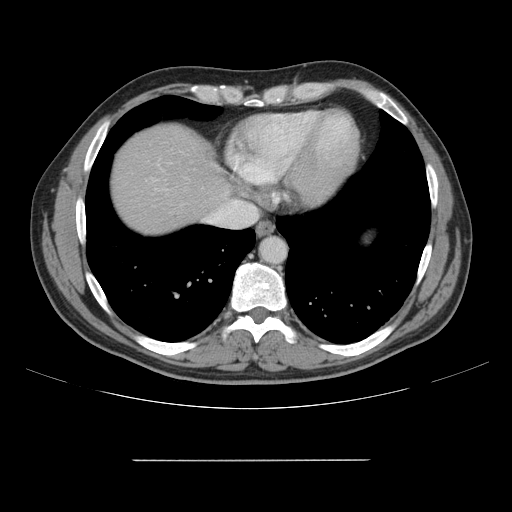
Contrast-enhanced abdominal CT, one axial slice; position 142 of 164 along the scan axis; 120 kVp; intravenous contrast given; soft-tissue window (W 400 / L 40 HU); 2.5 mm slice thickness; 512 × 512 image matrix, field of view 404 × 404 mm. Male patient, age 54 years. Case-level facts recorded for this patient, not image findings: diagnosis: colorectal cancer liver metastases, imaged before liver resection; multiple liver metastases: yes; largest metastasis: 1 cm.
Annotated regions visible in this slice (outlined manually by an expert reader):
- hepatic veins: bounding box <205,201,258,228> (left, top, right, bottom; pixels)
- liver: <111,124,231,235>
- planned liver remnant (the part of the liver to remain after resection): <111,124,229,235>